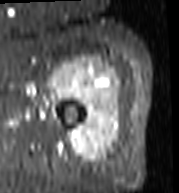
MRI of an extremity soft-tissue mass, one axial slice; position 83 of 103 along the scan axis; STIR; MR volume resampled by the dataset authors to the PET/CT grid (not the native acquisition matrix); 3.27 mm slice thickness; 179 × 193 image matrix, field of view 175 × 188 mm. Female patient. From the clinical record (not read from this slice): histological type: undifferentiated – high grade; grade: high; site of the primary tumour: left thigh.
Annotated regions visible in this slice (expert contour drawn on MRI and transferred to this co-registered scan by the dataset authors):
- gross tumour volume including surrounding oedema: bounding box (x1, y1, x2, y2) in pixels: (48, 57, 122, 164)
- gross tumour volume (mass): (50, 62, 122, 163)